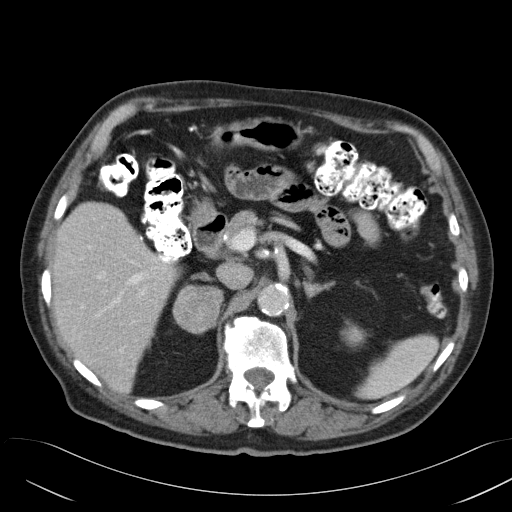
Contrast-enhanced abdominal CT, one axial slice. Reconstruction kernel B31f. 120 kVp. Intravenous contrast given. Soft-tissue window (W 400 / L 40 HU). 5 mm slice thickness. 512 × 512 image matrix. Patient: male, 82 years. From the clinical record (not read from this slice): diagnosis: adrenocortical carcinoma; tumour side: right adrenal; tumour size at pathology: 9 cm; Ki-67 index: 30 %; stage (as recorded): 3.
Annotated regions visible in this slice (semi-automatic segmentation, software-assisted and operator-edited):
- mass: bounding box (x1, y1, x2, y2) in pixels: (177, 289, 217, 330)